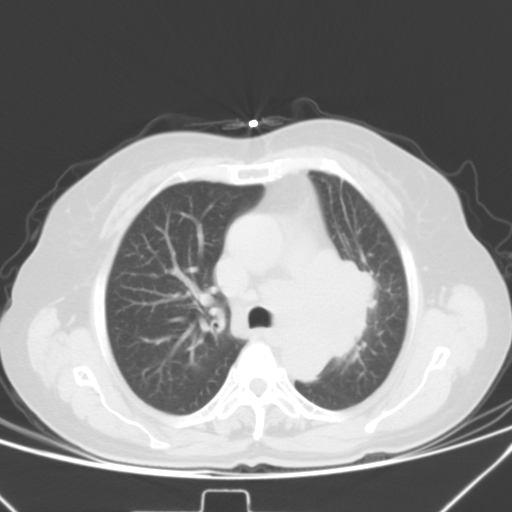
Chest CT, one axial slice. Position 29 of 42 along the scan axis. Lung window (W 1500 / L -600 HU). 5 mm slice thickness. 512 × 512 image matrix, field of view 331 × 331 mm. Patient: female, 59 years. From the clinical record (not read from this slice): clinical TNM (as recorded): T3 N1 M0; histopathological grade: G3.
Annotated regions visible in this slice (bounding box drawn by a radiologist):
- lung tumour (recorded histology: small cell carcinoma): bounding box [x1, y1, x2, y2] px = [328, 239, 398, 371]